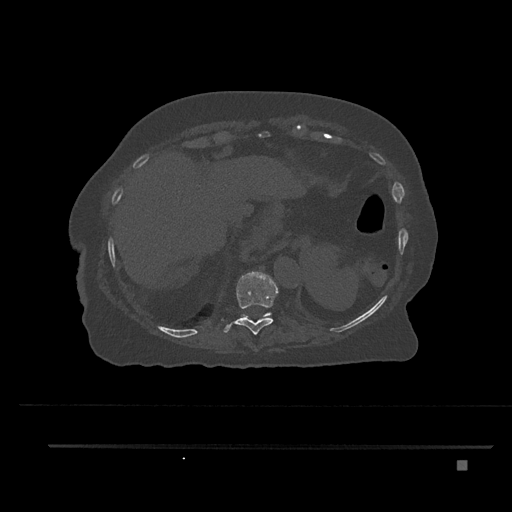
CT including the spine, one axial slice; 120 kVp; bone window (W 1800 / L 400 HU); 512 × 512 image matrix. Patient: female, 76 years. From the clinical record (not read from this slice): primary cancer: lung; vertebrae with lytic lesions (as recorded): T11, L3.
Structures marked on this image (semi-automatic segmentation, software-assisted and operator-edited):
- T10 vertebra: bounding box [x1, y1, x2, y2] px = [222, 272, 278, 335]
- T11 vertebra: [241, 313, 271, 317]